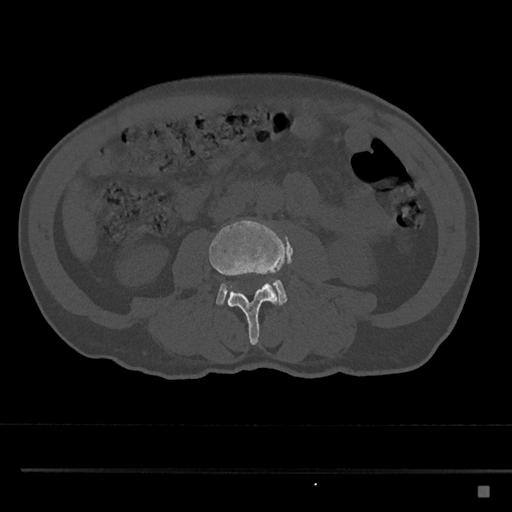
CT including the spine, one axial slice. Slice 678 of 797 in the series (ordered by position). Reconstruction kernel Br40s/3. Bone window (W 1800 / L 400 HU). 512 × 512 image matrix, field of view 391 × 391 mm. Patient: male, 59 years. From the clinical record (not read from this slice): primary cancer: prostate.
Outlined on this slice (semi-automatic segmentation, software-assisted and operator-edited):
- L3 vertebra: box from (x=209, y=219) to (x=287, y=345) px
- L4 vertebra: (x=216, y=279)–(x=288, y=306)